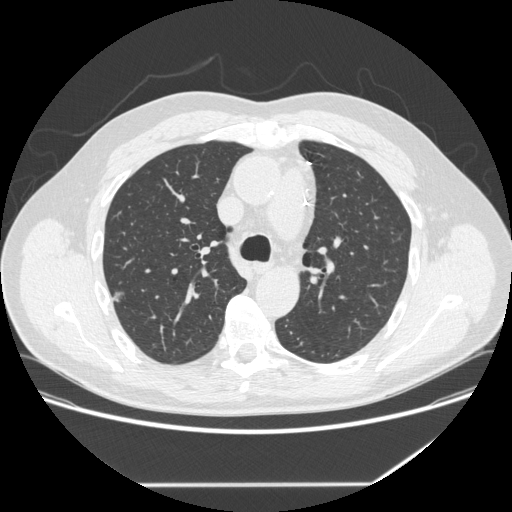
Chest CT (low-dose screening protocol), one axial image; baseline screening round; lung window (W 1500 / L -600 HU); 1.25 mm slice thickness; standard (soft-tissue) reconstruction kernel (STANDARD); slice 89 of 262 in the series. Male, age 62 years at enrolment. Current smoker at enrolment.
Expert reader's lesion annotation, bounding box (x1, y1, x2, y2) in pixels: (101, 280, 131, 314). No non-calcified nodule or mass ≥4 mm was recorded by the screening reader at this exam. Official screen result: negative screen, minor abnormalities not suspicious for lung cancer.